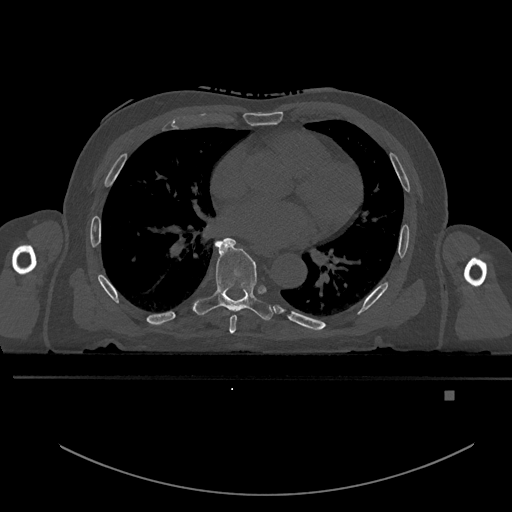
CT including the spine, one axial slice; slice 263 of 969 in the series (ordered by position); bone window (W 1800 / L 400 HU); 512 × 512 image matrix, field of view 456 × 456 mm. Male patient, age 82 years. From the clinical record (not read from this slice): primary cancer: prostate.
Annotated regions visible in this slice (semi-automatically segmented with operator editing):
- T6 vertebra: bounding box [x1, y1, x2, y2] px = [229, 315, 237, 334]
- T7 vertebra: [192, 238, 273, 321]